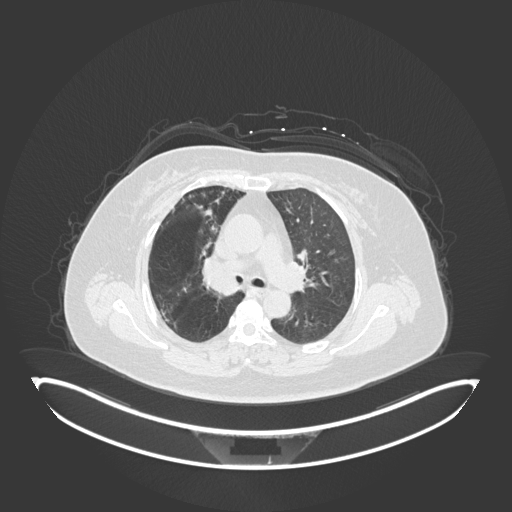
Chest CT, one axial slice; position 110 of 245 along the scan axis; reconstruction kernel B30f; 120 kVp; lung window (W 1500 / L -600 HU); 1 mm slice thickness; 512 × 512 image matrix, field of view 500 × 500 mm. Female patient, age 60 years. Case-level facts recorded for this patient, not image findings: clinical TNM (as recorded): T1c N0 M0; histopathological grade: G1-G2.
Outlined on this slice (bounding box drawn by a radiologist):
- lung tumour (recorded histology: squamous cell carcinoma): box from (x=198, y=254) to (x=240, y=300) px